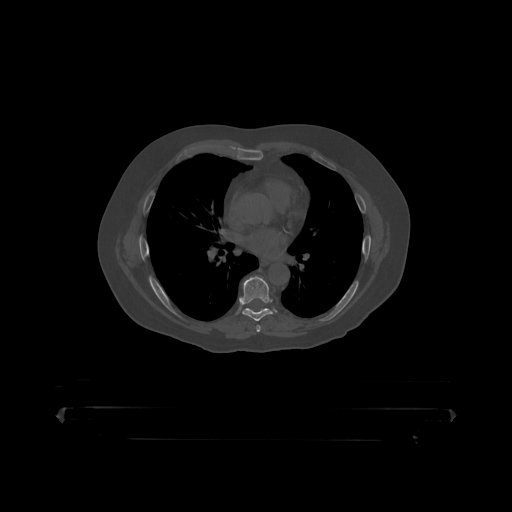
CT including the spine, one axial slice. Position 278 of 390 along the scan axis. Bone window (W 1800 / L 400 HU). 1.25 mm slice thickness. 512 × 512 image matrix. Patient: male, 60 years. Case-level facts recorded for this patient, not image findings: primary cancer: prostate.
Structures marked on this image (semi-automatically segmented with operator editing):
- T7 vertebra: box from (x=240, y=277) to (x=276, y=319) px
- T8 vertebra: (x=265, y=308)–(x=267, y=310)